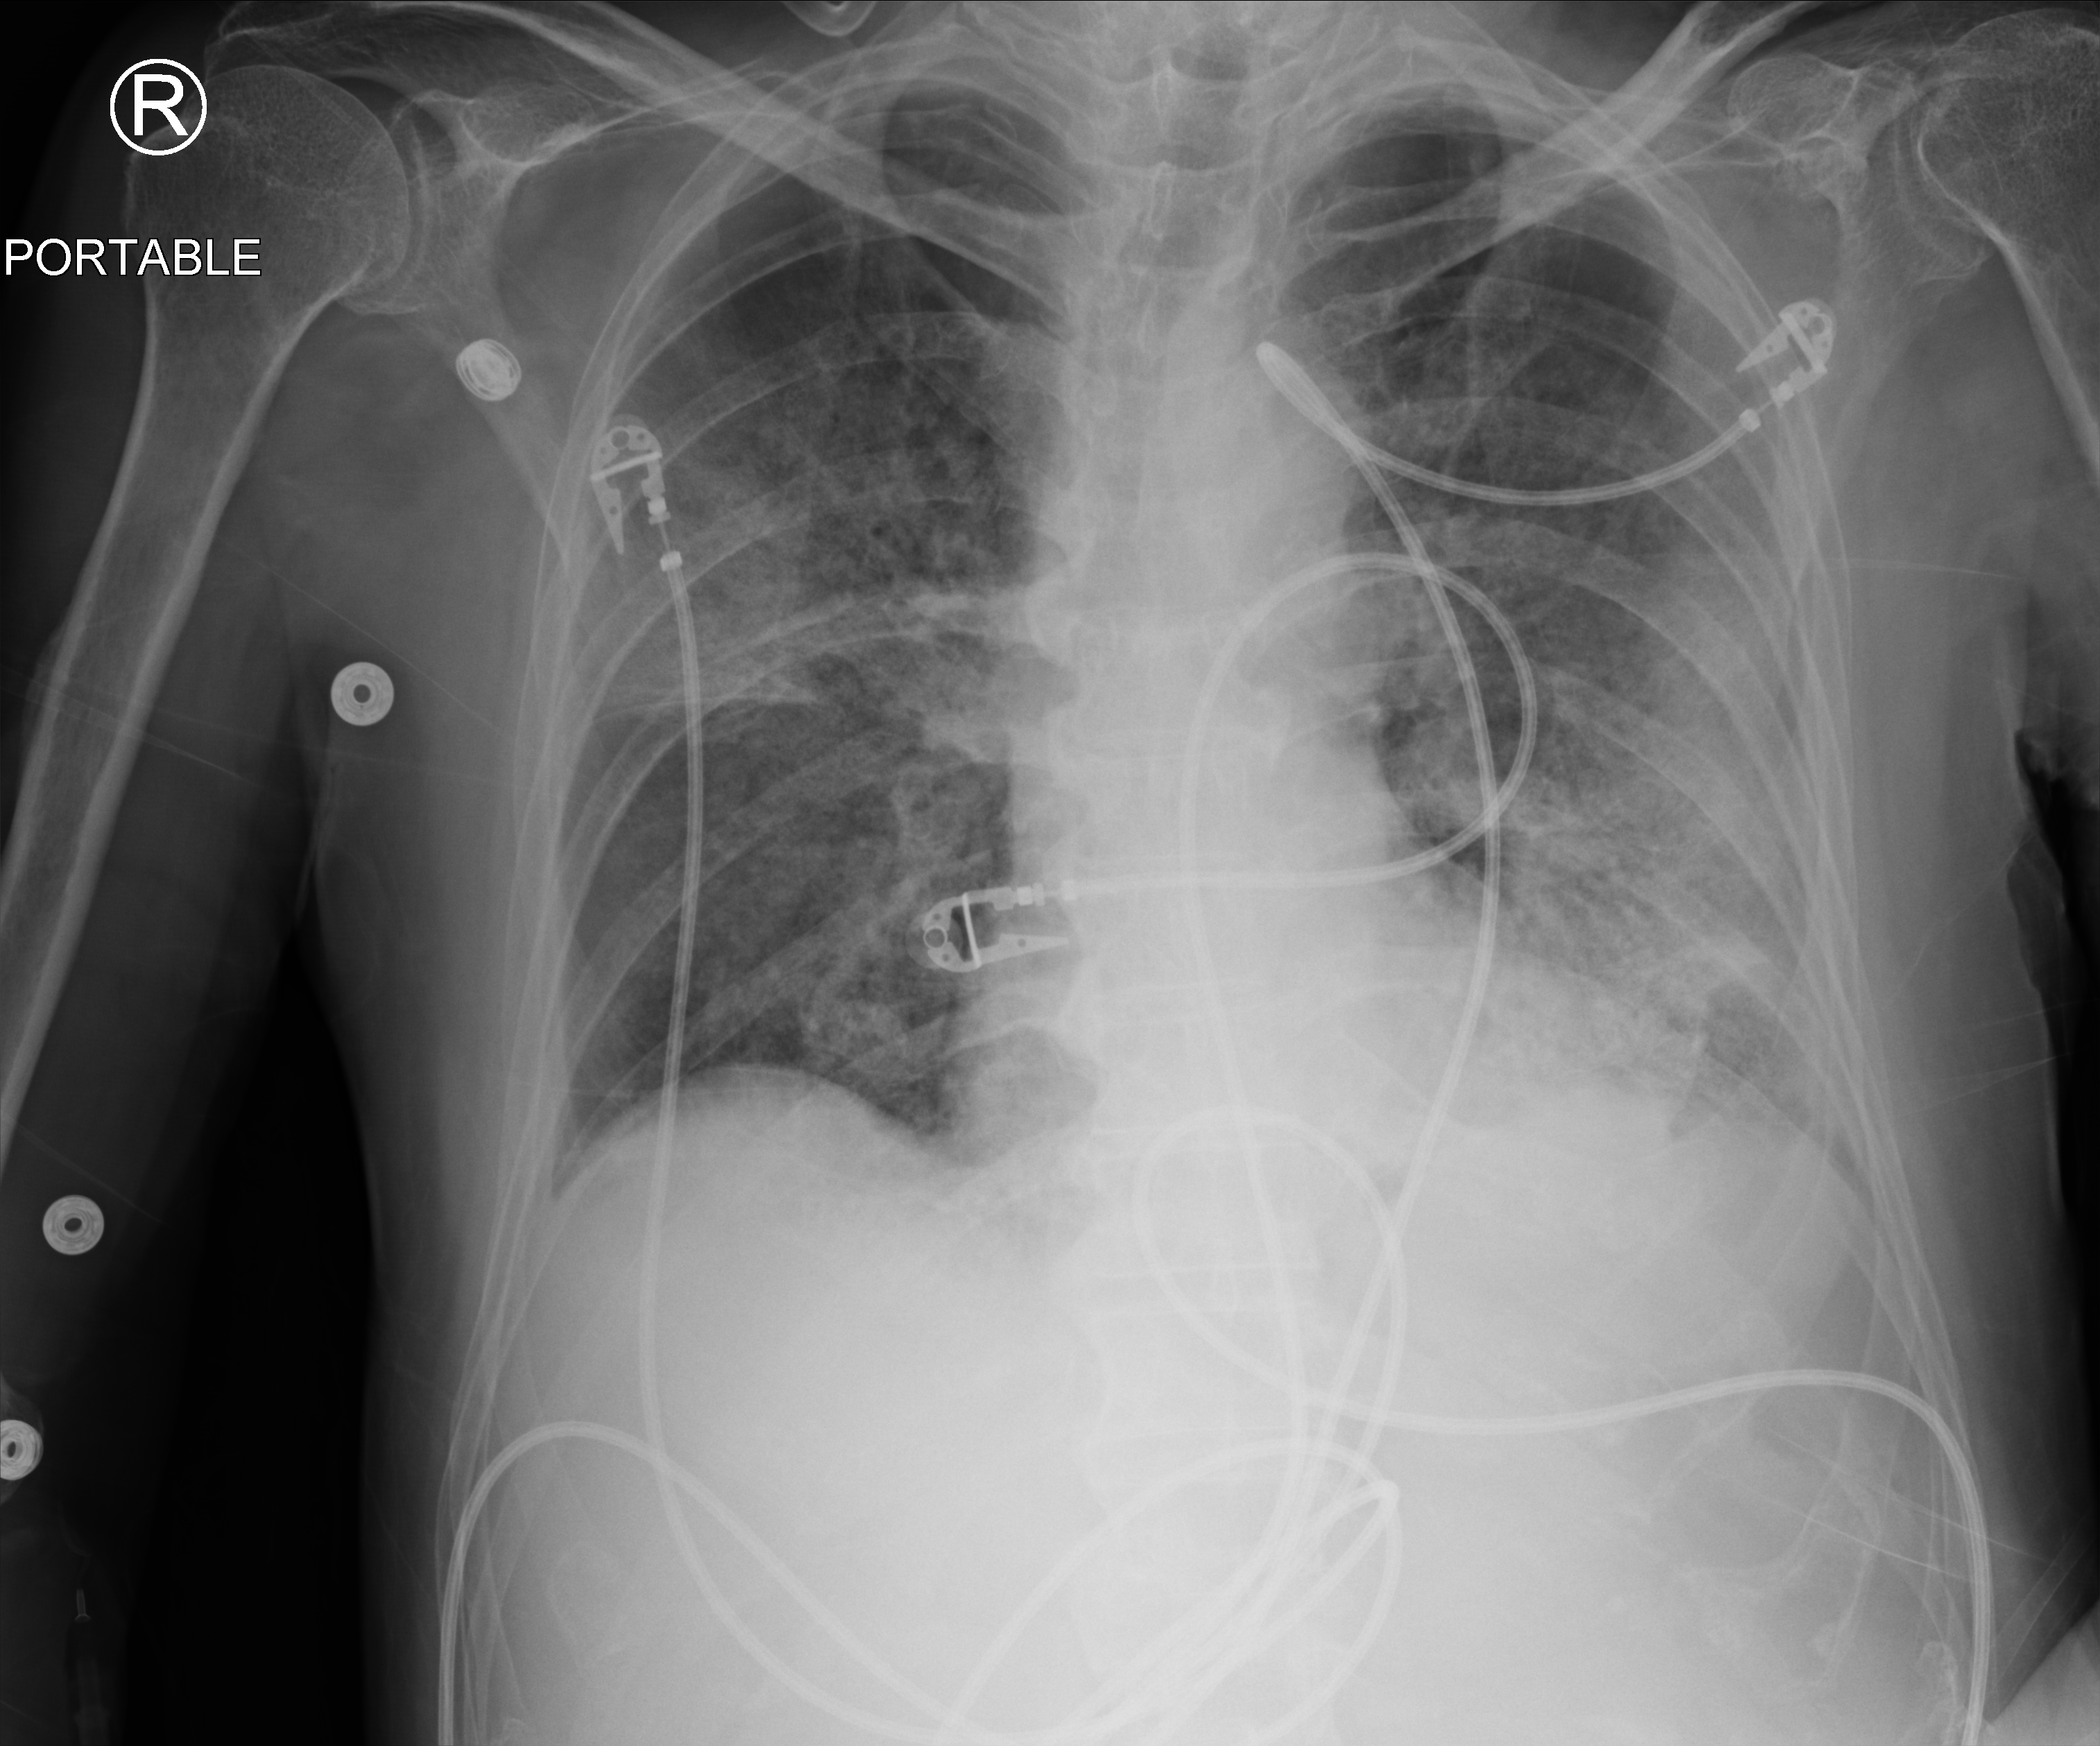
Portable chest radiograph; anteroposterior (AP) projection. Patient hospitalised with COVID-19; male, aged 60–74 years.
From the hospital-stay record, not from the radiograph (when in the stay this image was taken is not recorded): COPD (admission record): no; mechanically ventilated during this hospital stay: yes; admitted to intensive care during this hospital stay: yes.